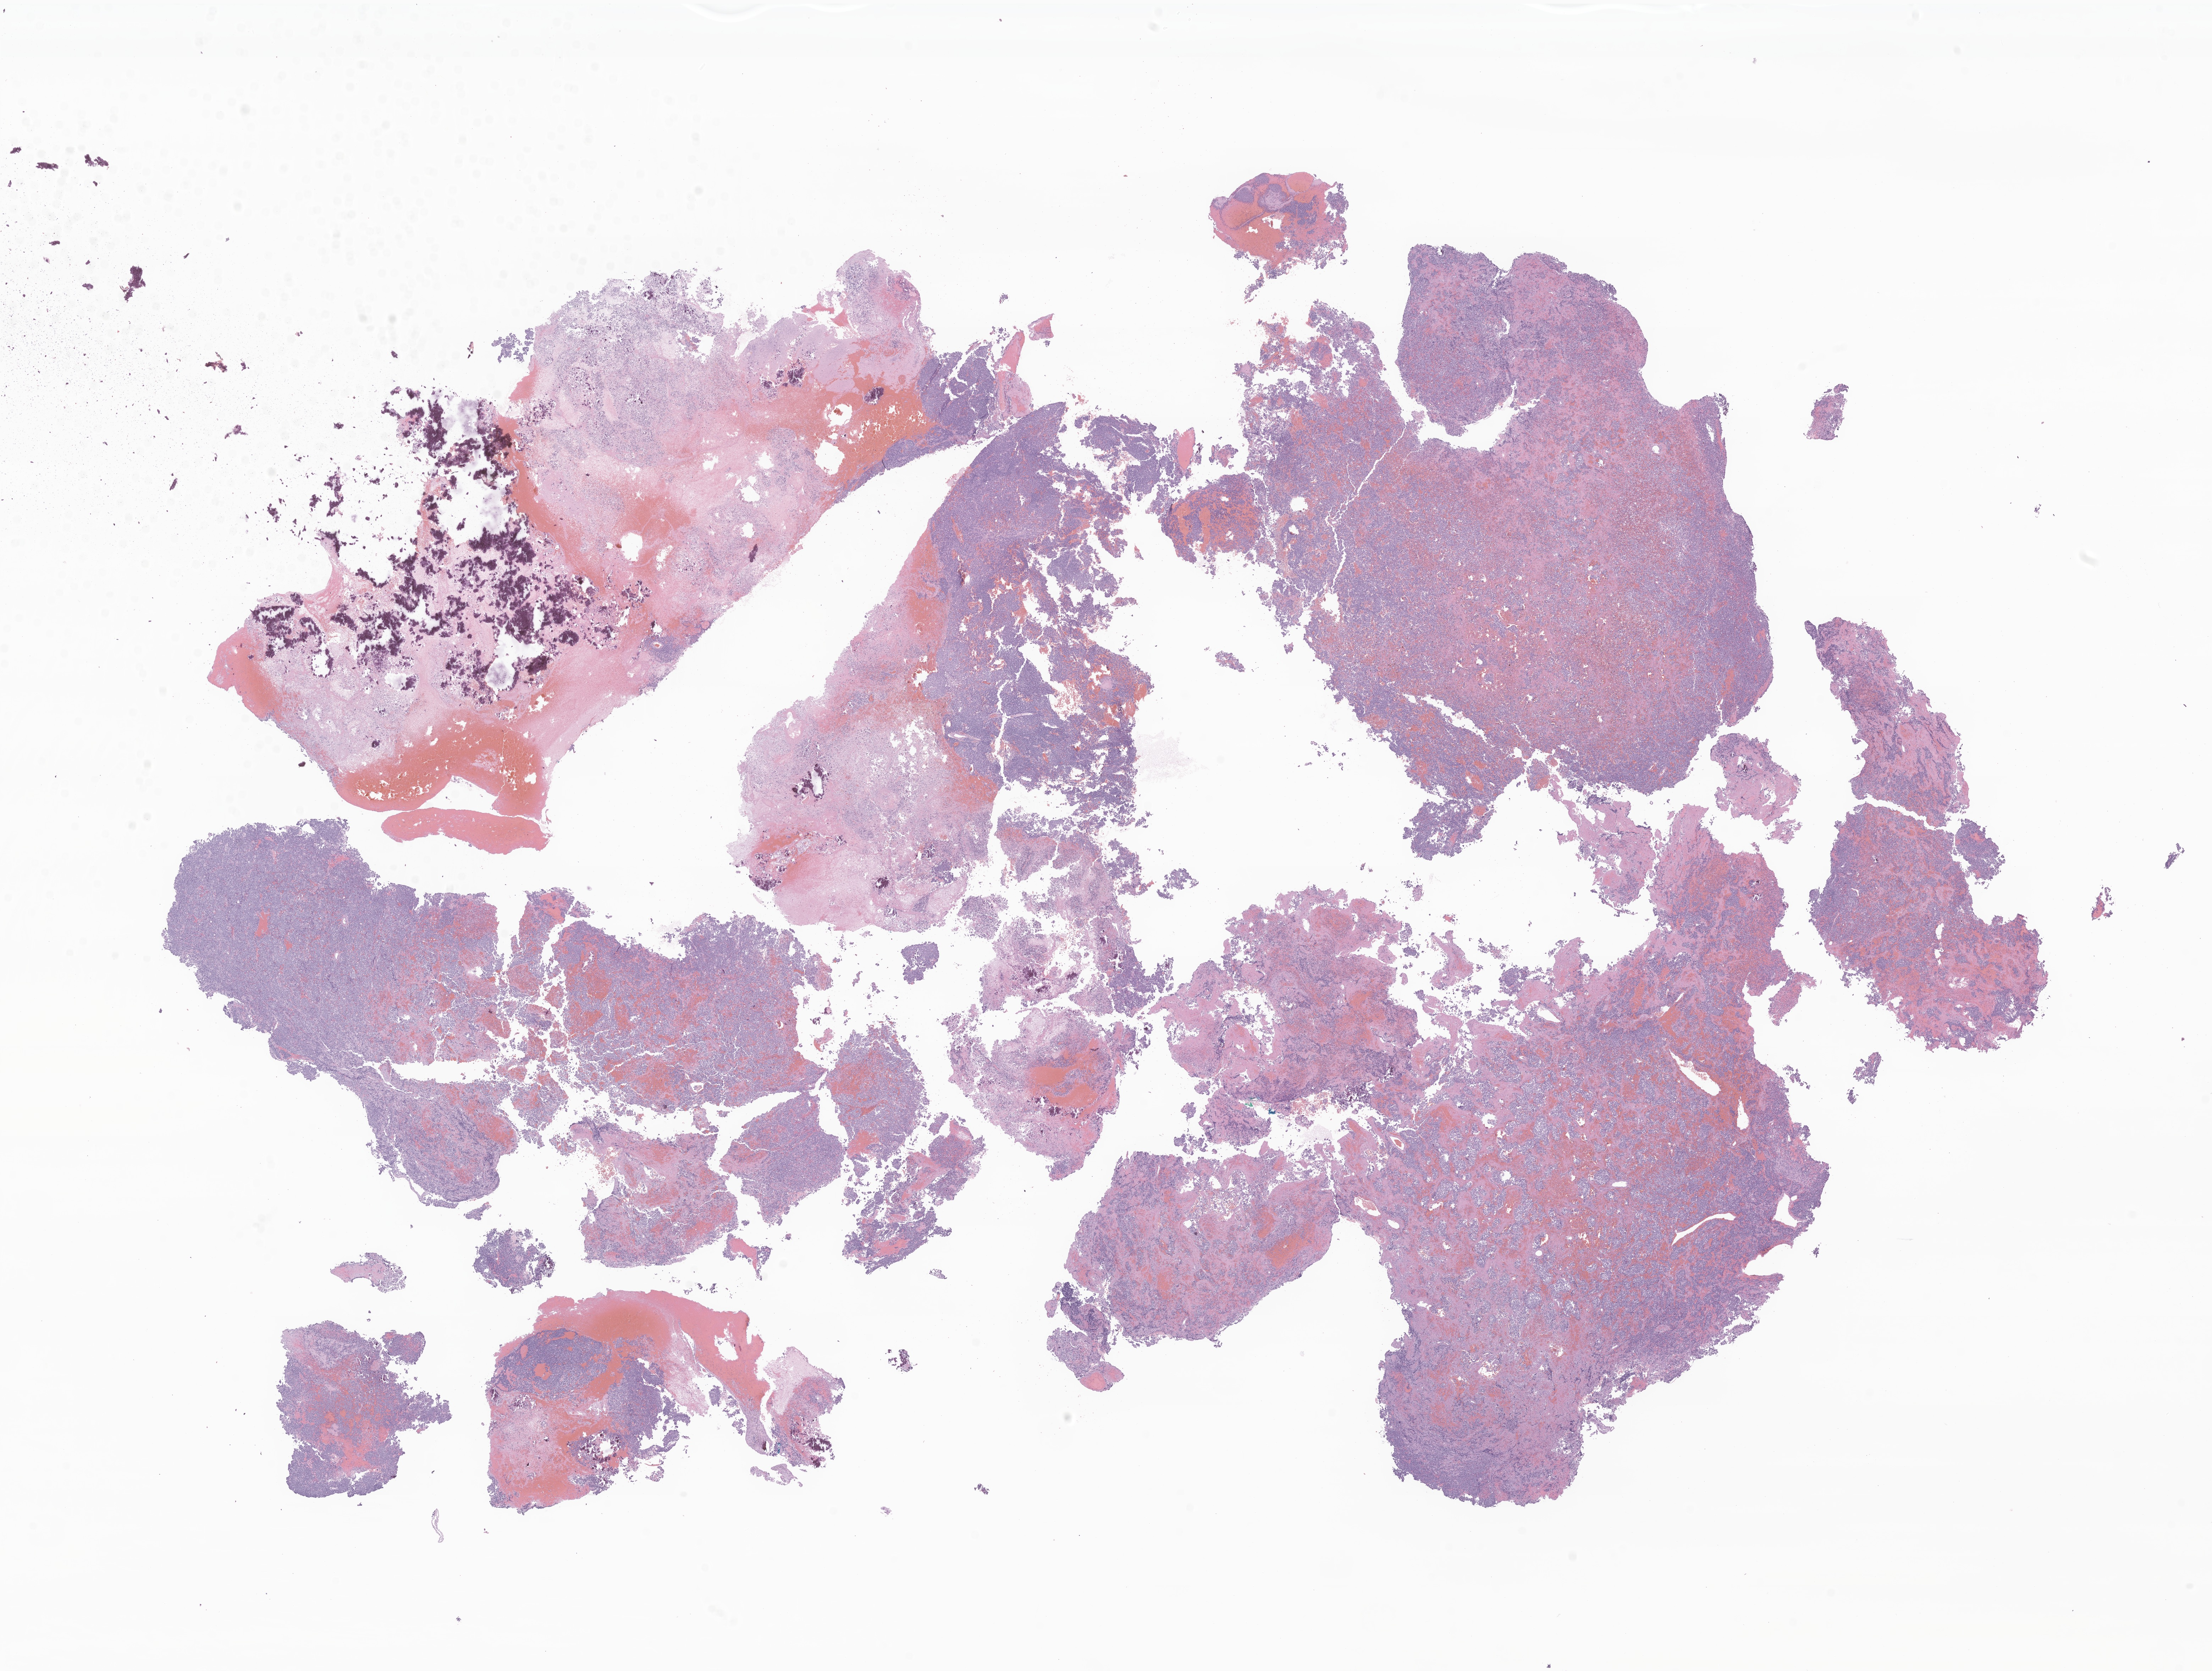
Digitized H&E-stained section of tumor tissue from the brain, shown as a low-resolution overview of the whole scanned area (about 26.3 x 19.9 mm); FFPE section. Patient female; age 63 months (5 years 3 months).
* diagnosis (ICD-O-3 morphology term): Pineoblastoma